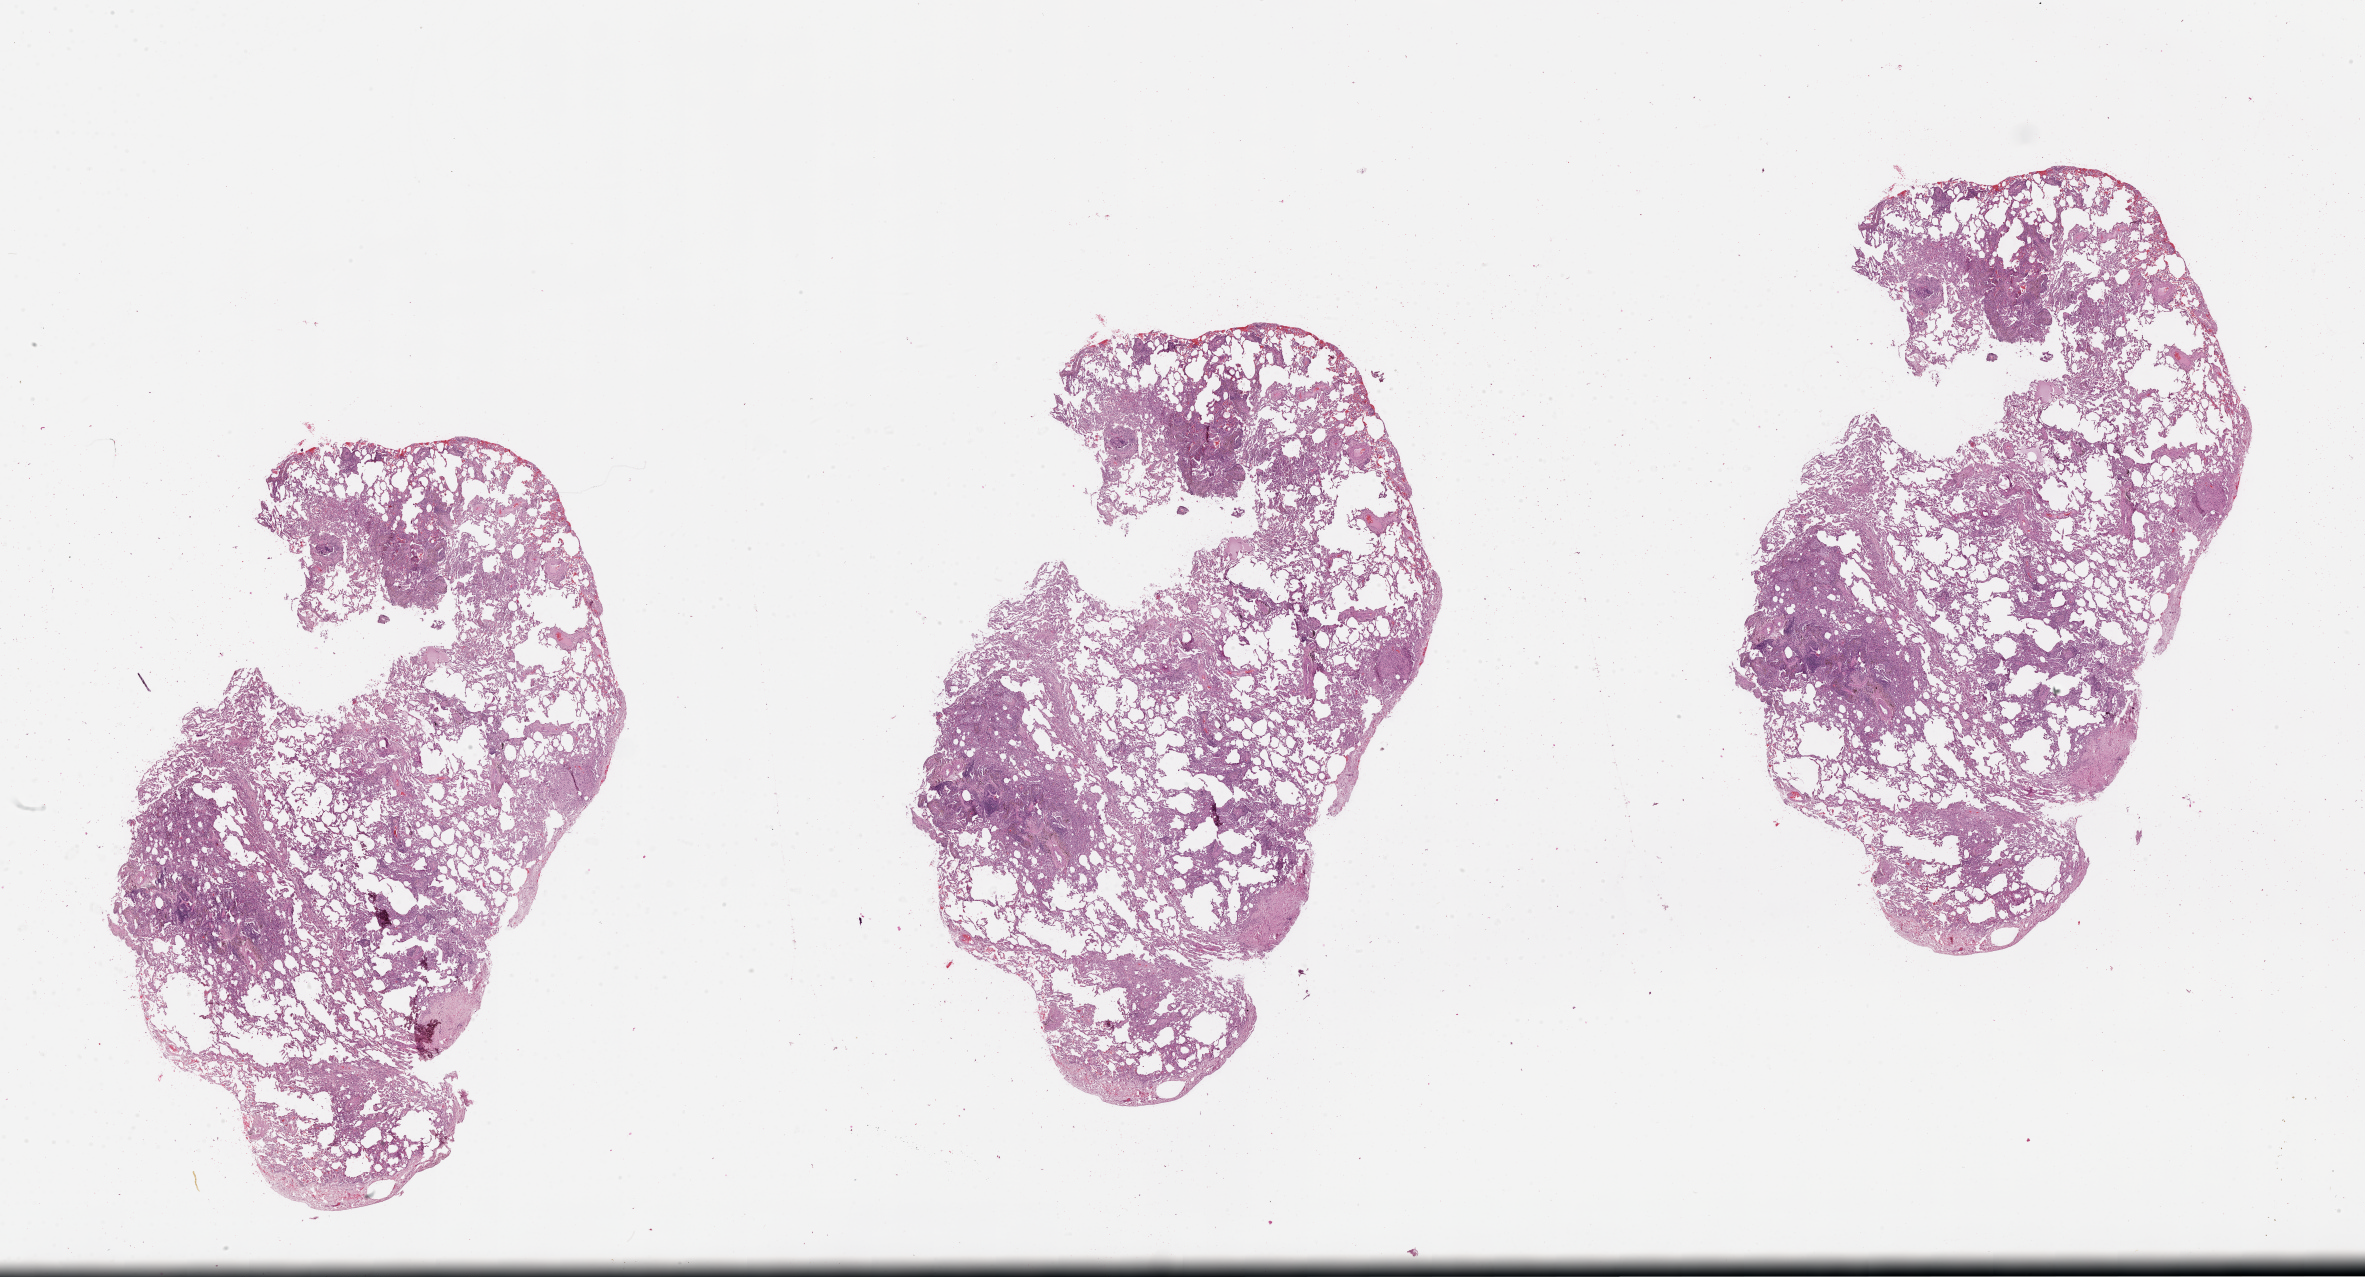
Hematoxylin and eosin (H&E) stained whole-slide image, low-resolution overview of the scanned area, about 38.1 x 20.6 mm (slide scanned at 20x). Lung, normal (non-tumour) tissue. Male, 43 y/o.
This section: normal (non-tumour) tissue from the same patient. Patient diagnosis (cohort enrolment): squamous cell carcinoma (lung).